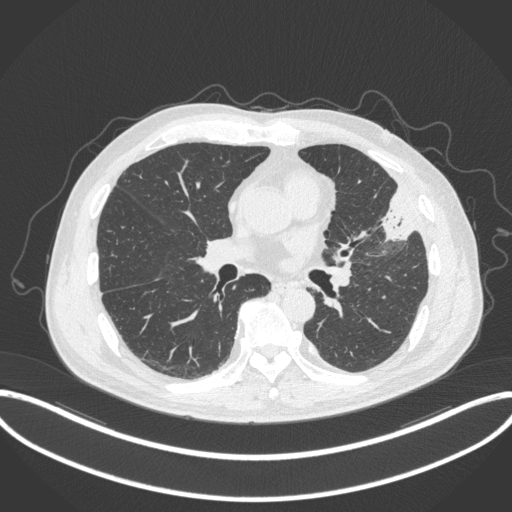
Chest CT, one axial slice; slice 172 of 382 in the series (ordered by position); lung window (W 1500 / L -600 HU); 1 mm slice thickness; 512 × 512 image matrix, field of view 415 × 415 mm. Male patient, age 64 years. From the clinical record (not read from this slice): clinical TNM (as recorded): T4 N1 M0; histopathological grade: G3.
Outlined on this slice (rectangle marked by the reading radiologist):
- lung tumour (recorded histology: adenocarcinoma): box from (x=377, y=182) to (x=419, y=248) px